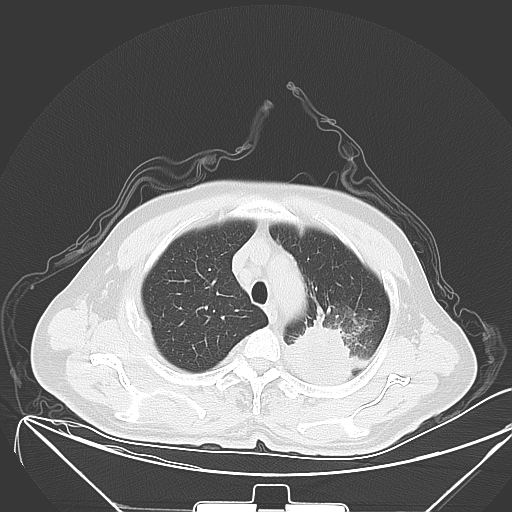
Chest CT, one axial slice; slice 48 of 64 in the series (ordered by position); 120 kVp; lung window (W 1500 / L -600 HU); 5 mm slice thickness; 512 × 512 image matrix, field of view 431 × 431 mm. Male patient, age 58 years. From the clinical record (not read from this slice): clinical TNM (as recorded): T2b N3 M1b; histopathological grade: G3.
Structures marked on this image (bounding box drawn by a radiologist):
- lung tumour (recorded histology: adenocarcinoma): box from (x=287, y=315) to (x=355, y=387) px